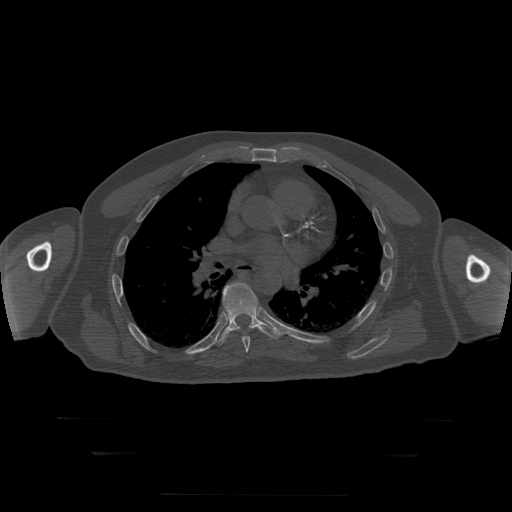
CT including the spine, one axial slice; slice 175 of 397 in the series (ordered by position); reconstruction kernel STANDARD; bone window (W 1800 / L 400 HU); 1.25 mm slice thickness; 512 × 512 image matrix, field of view 510 × 510 mm. Patient age 73 years. From the clinical record (not read from this slice): primary cancer: prostate.
Outlined on this slice (semi-automatically segmented with operator editing):
- T7 vertebra: bounding box [x1, y1, x2, y2] px = [242, 336, 250, 353]
- T8 vertebra: [212, 283, 284, 346]